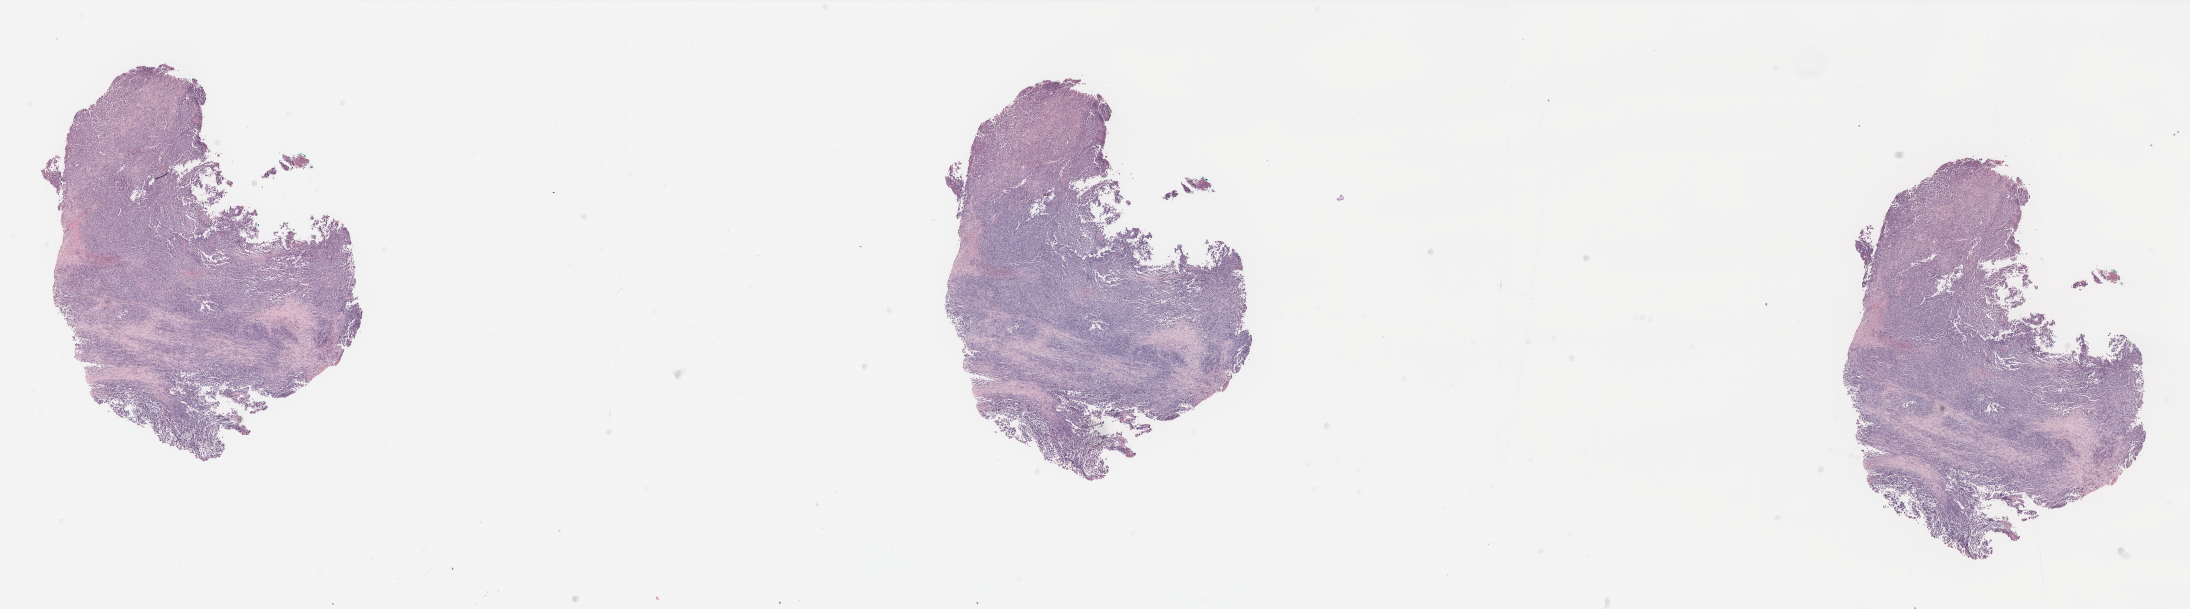
Digitized H&E-stained tissue section (whole slide) — low-resolution overview of the scanned area, about 35.1 x 9.8 mm, FFPE section, skin, primary tumour sample. Patient: female, age at initial diagnosis 32 years.
Diagnosis: Malignant melanoma, NOS.